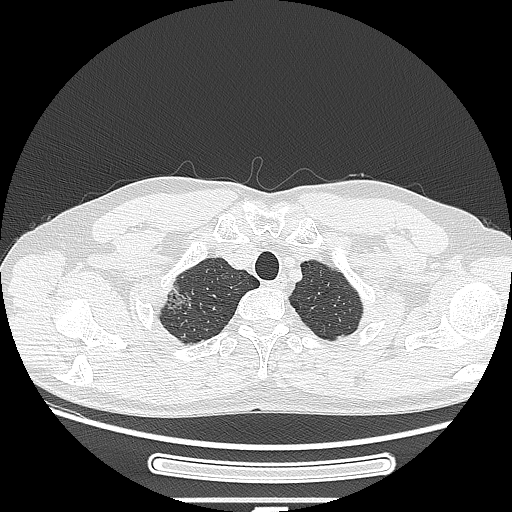
Chest CT, one axial slice; slice 237 of 269 in the series (ordered by position); 120 kVp; lung window (W 1500 / L -600 HU); 1.25 mm slice thickness; 512 × 512 image matrix, field of view 382 × 382 mm. Male patient, age 53 years. From the clinical record (not read from this slice): clinical TNM (as recorded): T1c N0 M0.
Structures marked on this image (bounding box drawn by a radiologist):
- lung tumour (recorded histology: adenocarcinoma): bounding box [x1, y1, x2, y2] px = [157, 279, 201, 324]